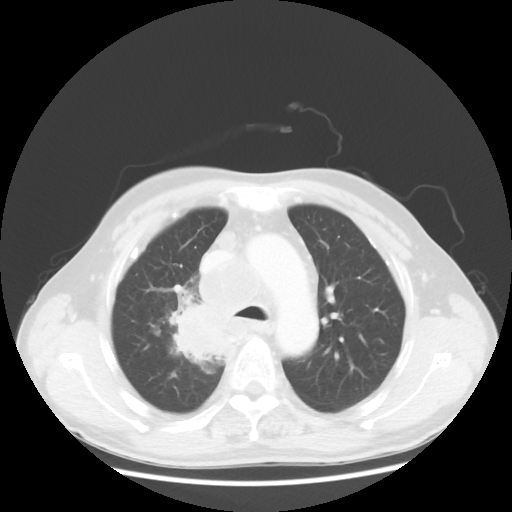
Chest CT, one axial slice; slice 88 of 124 in the series (ordered by position); lung window (W 1500 / L -600 HU); 512 × 512 image matrix, field of view 382 × 382 mm. Male patient, age 64 years. From the clinical record (not read from this slice): clinical TNM (as recorded): T3 N3 M0; histopathological grade: G3.
Outlined on this slice (bounding box drawn by a radiologist):
- lung tumour (recorded histology: small cell carcinoma): bounding box <167,292,232,378> (left, top, right, bottom; pixels)